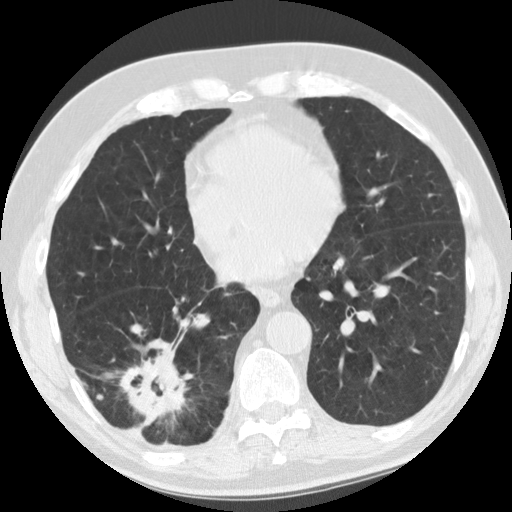
Chest CT (low-dose screening protocol), one axial image. Baseline annual screen. Lung window (W 1500 / L -600 HU). 120 kVp. Slice 89 of 135 in the series. 512 × 512 image matrix, field of view 340 × 340 mm. Male participant, aged 69 years at enrolment. Former smoker at enrolment.
• Expert reader's lesion annotation, bounding box [x1, y1, x2, y2] px = [107, 331, 193, 440].
• The screening reader recorded 2 non-calcified nodules or masses ≥4 mm on this exam (right lower lobe, right lower lobe); which of them this box marks is not recorded.
• Participant outcome: lung cancer diagnosed 40 days after this screen — adenocarcinoma, NOS, right lower lobe, stage IIB (AJCC 6th edition), 45 mm at pathology.